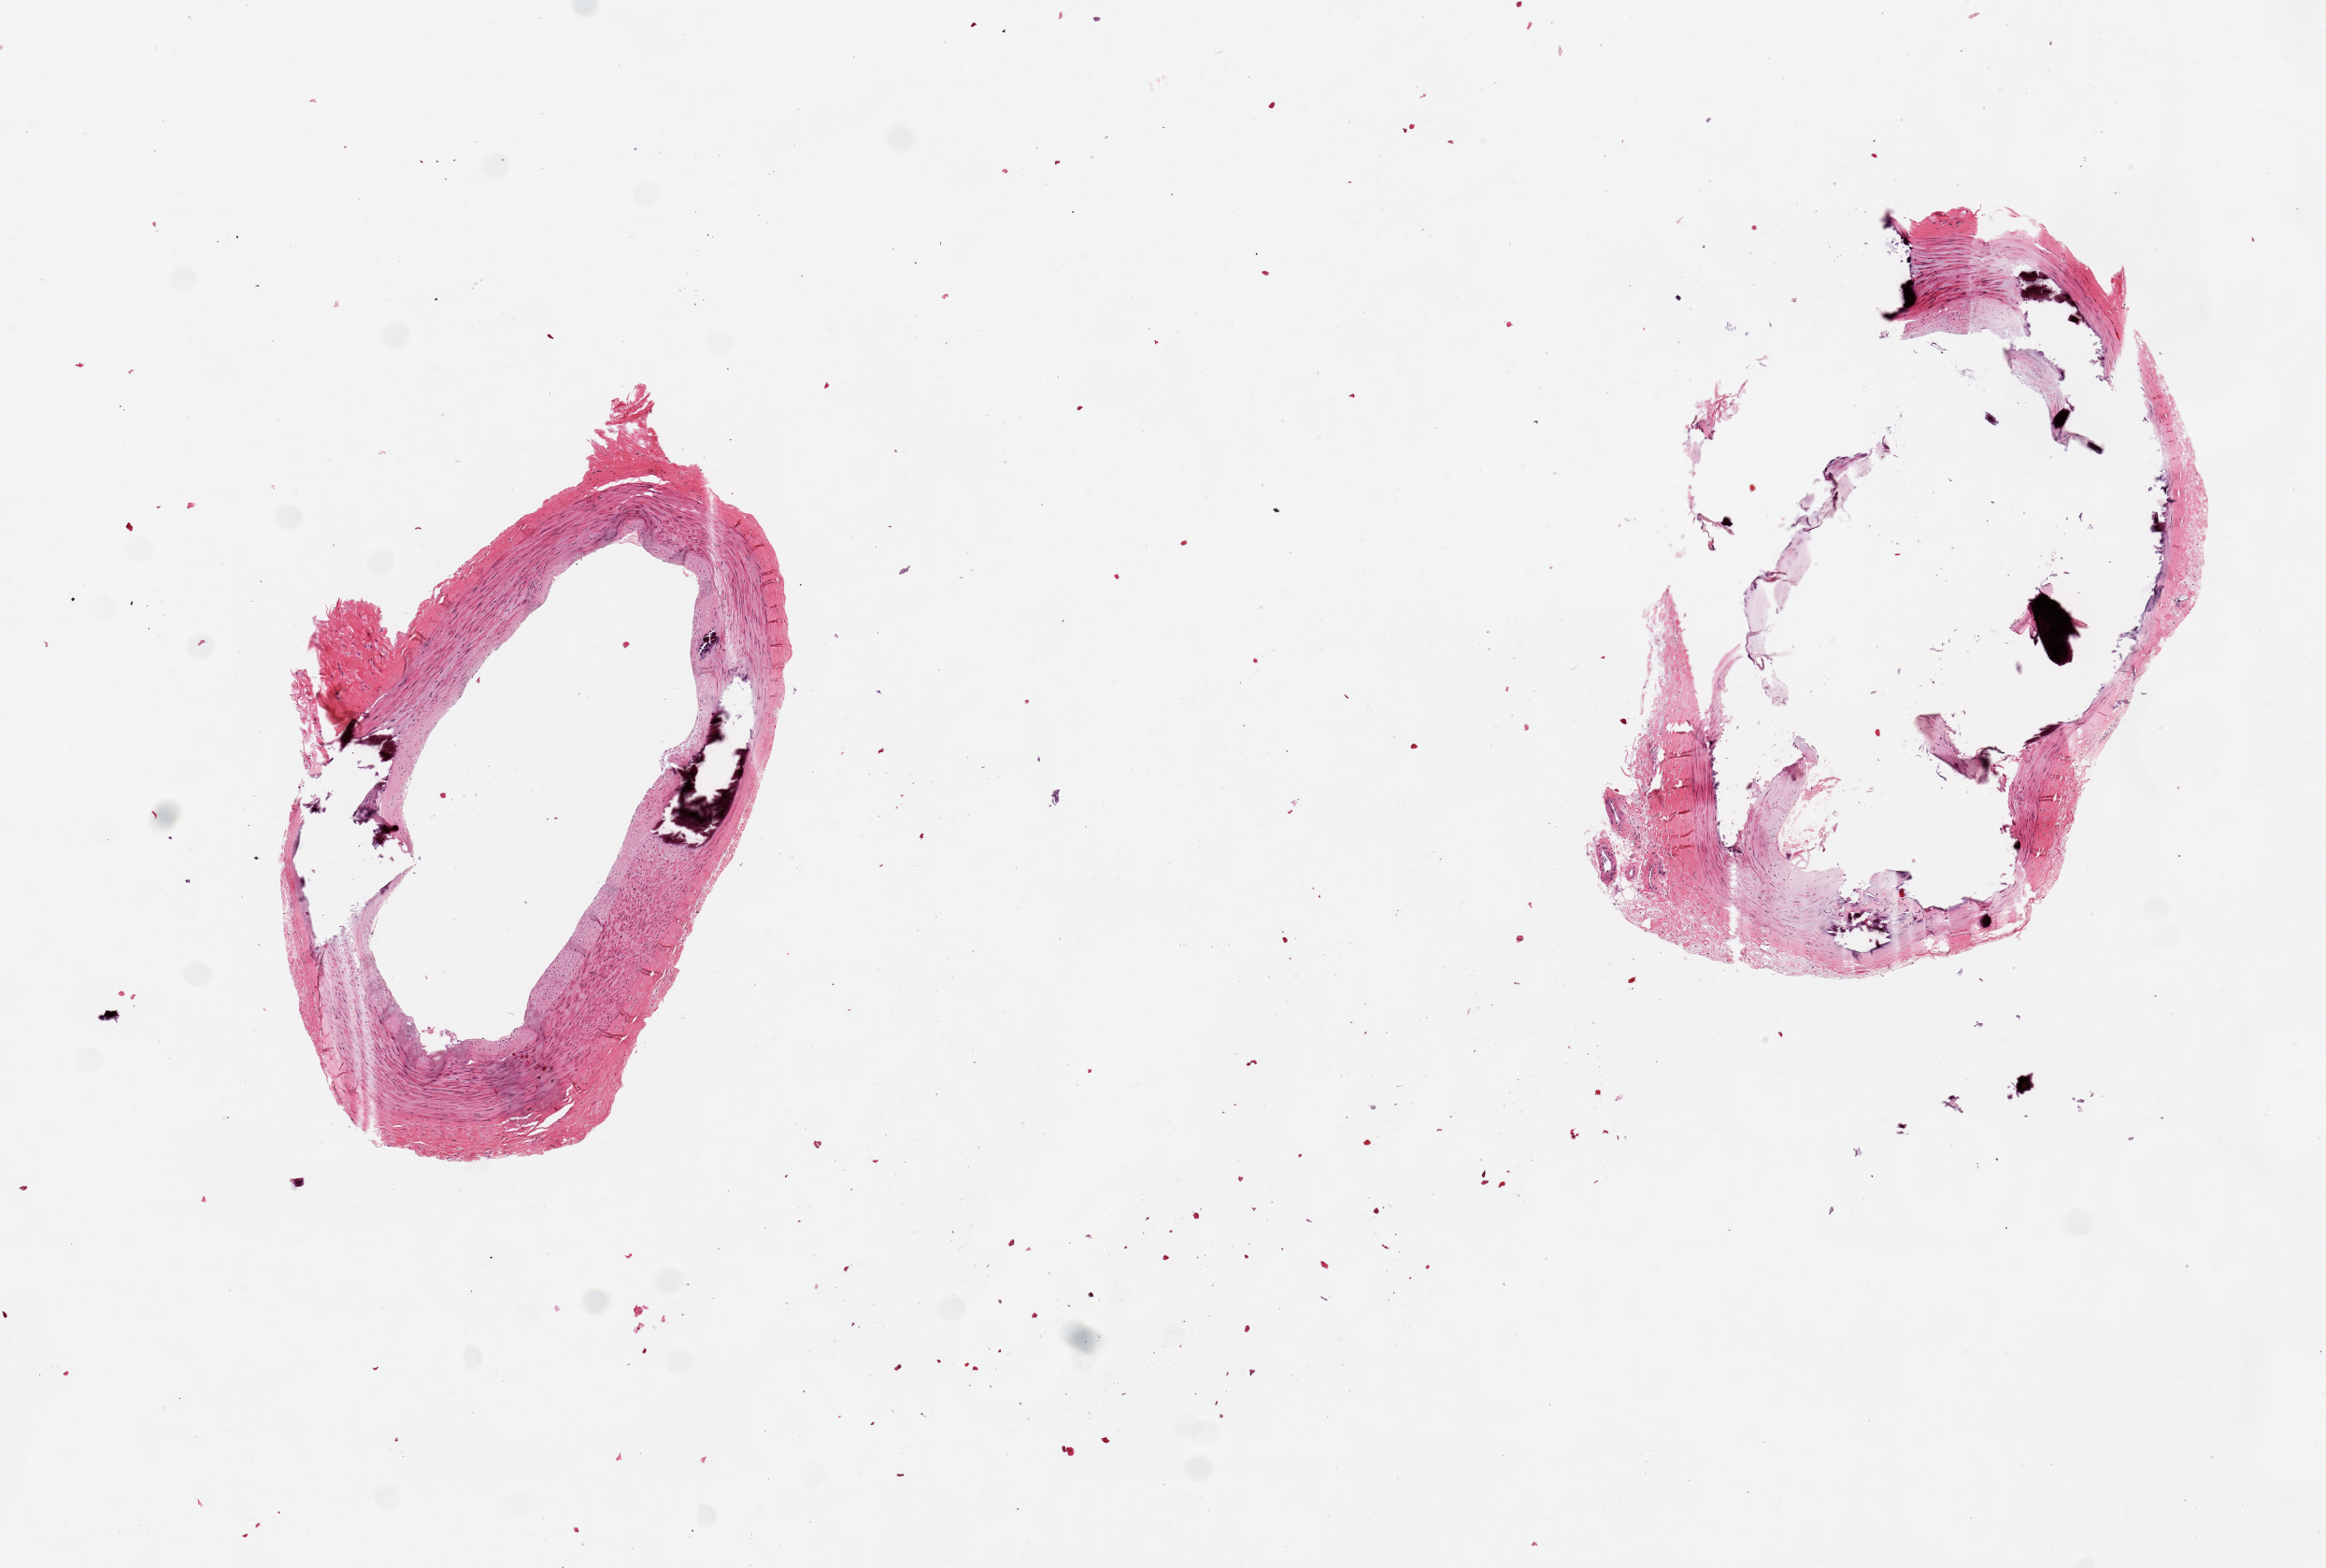
Digitized H&E-stained section, shown as a low-resolution overview of the whole scanned area (about 9.8 x 6.6 mm). PAXgene-fixed paraffin-embedded (PFPE) section. Sampled site (target tissue): tibial artery. Donor tissue sample.
Reviewer comment on this tissue sample: 2 pieces, 3x2 & 3x2mm; Heavily calcified.